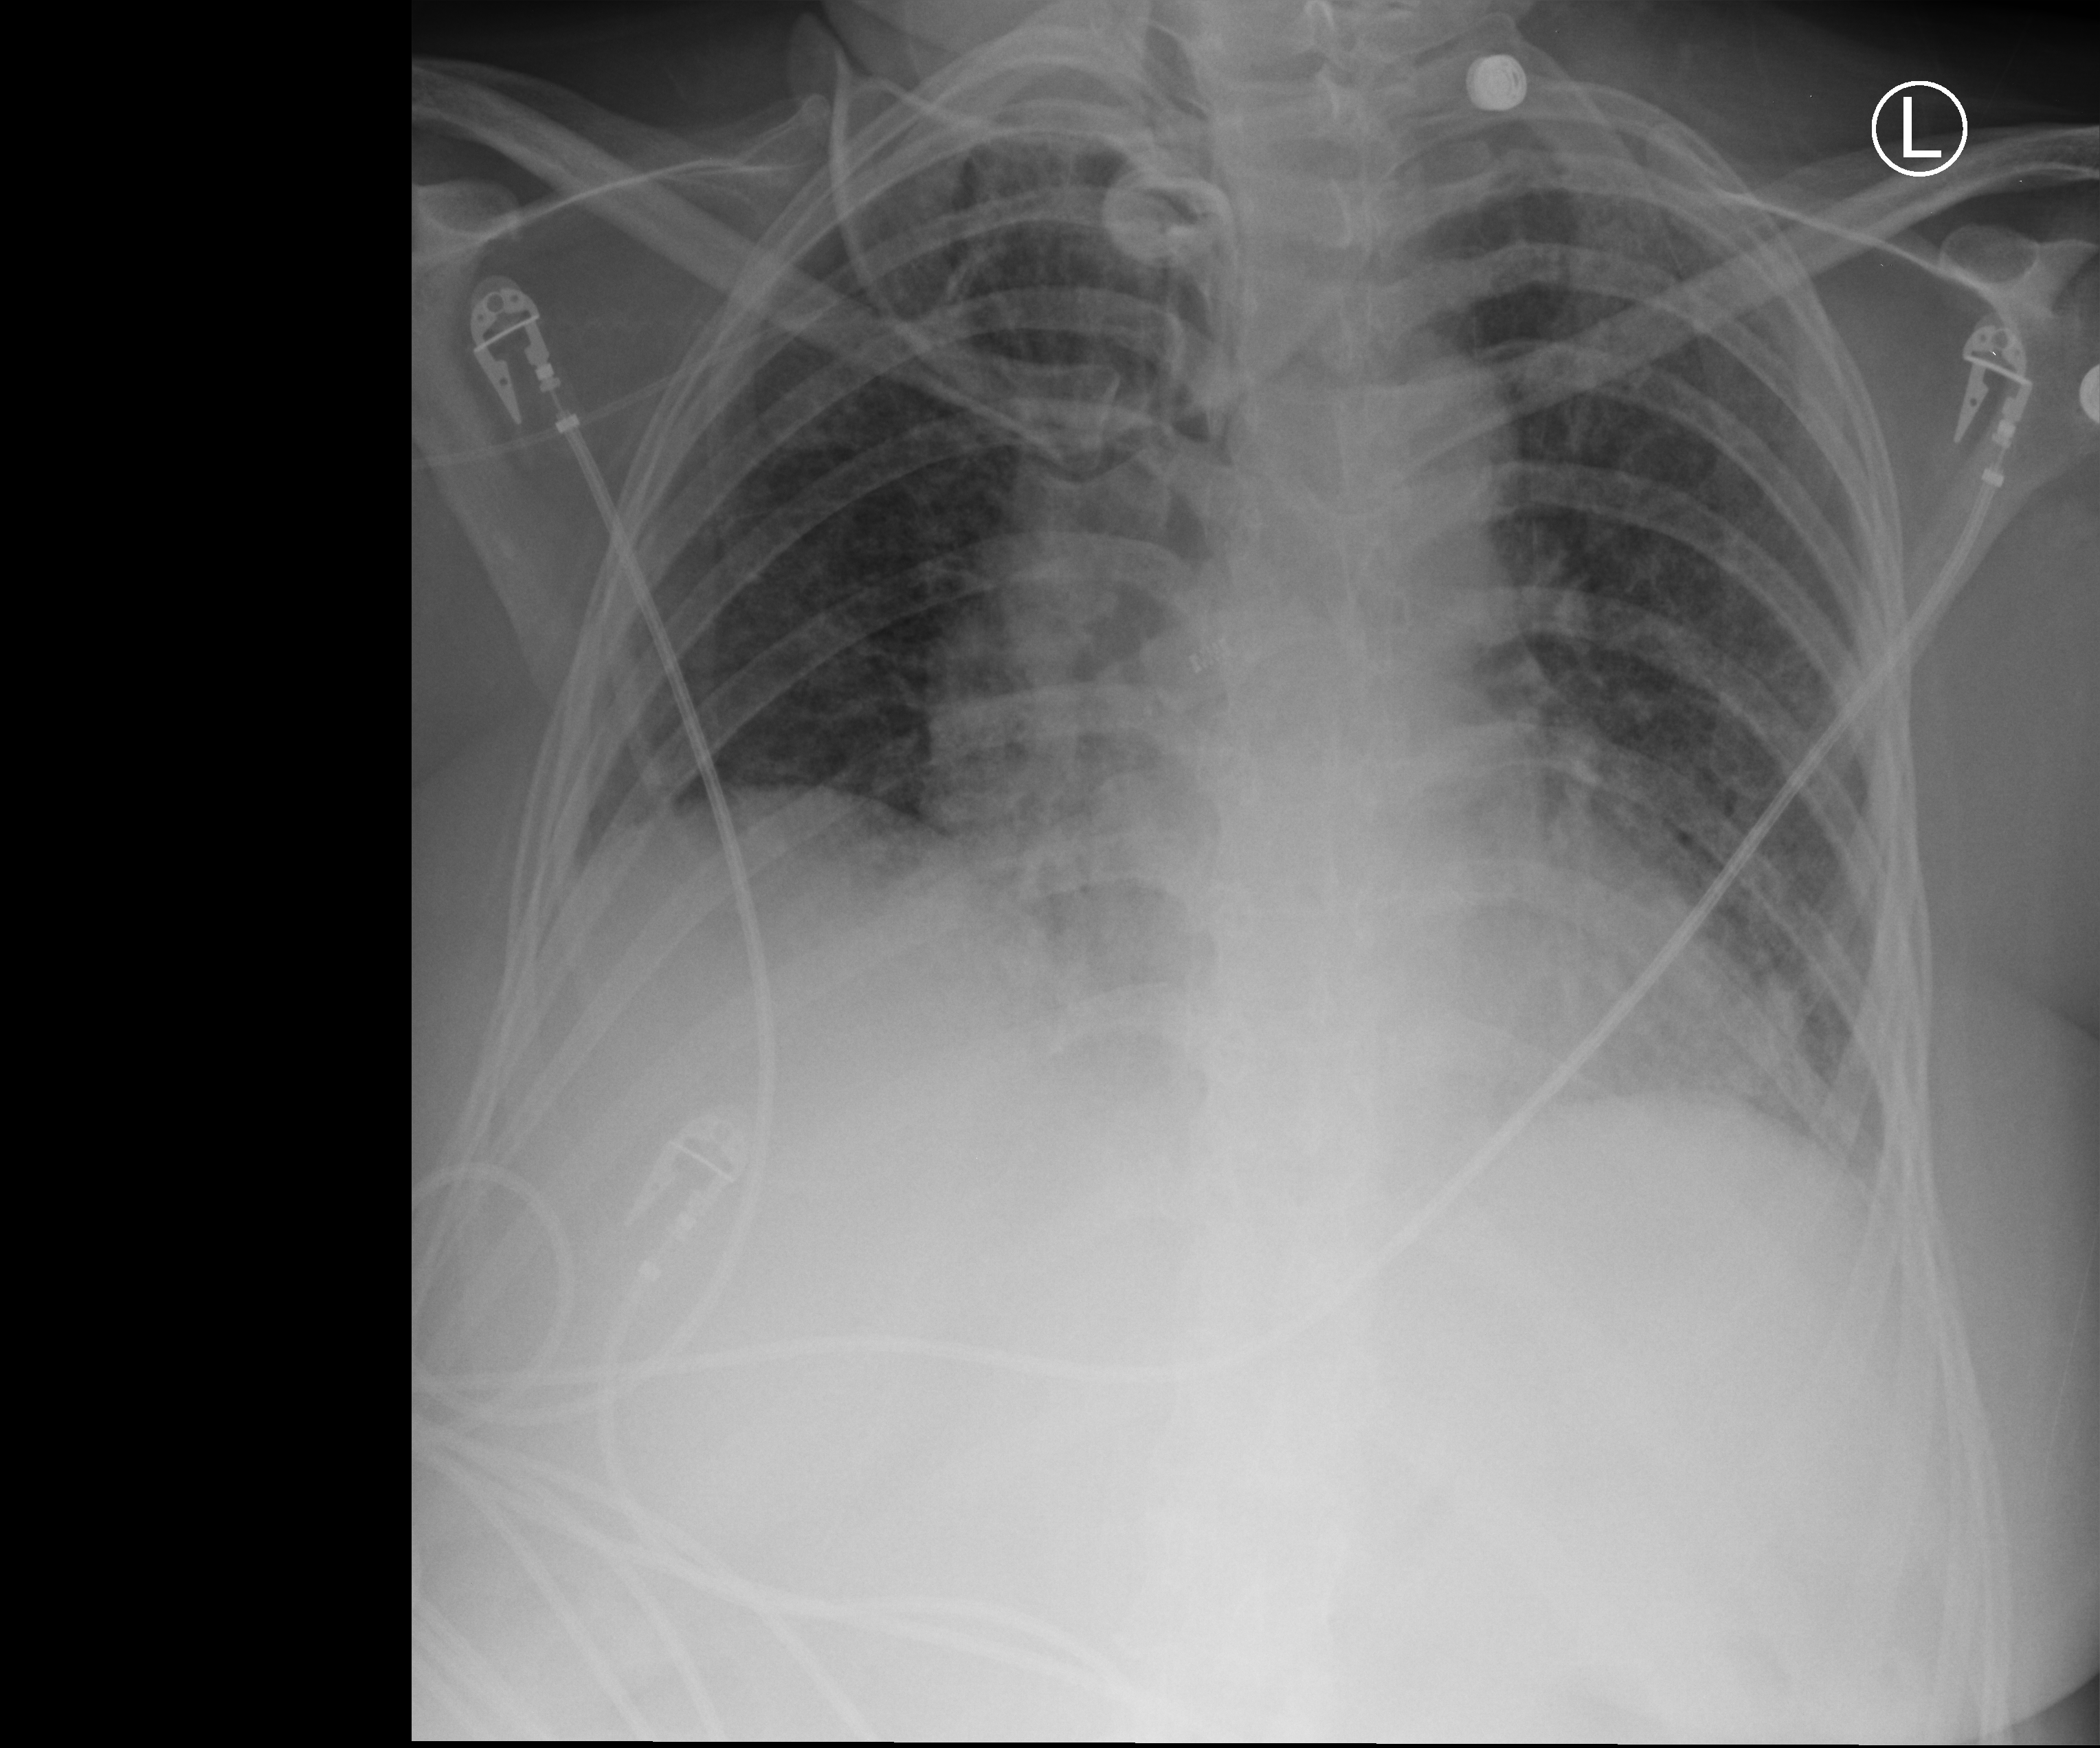
Chest X-ray (portable), anteroposterior (AP) projection. Patient hospitalised with COVID-19; female, aged 18–59 years.
Hospital-stay facts (about this admission, not read from this image; timing relative to this image not recorded):
- admitted to intensive care during this hospital stay: yes